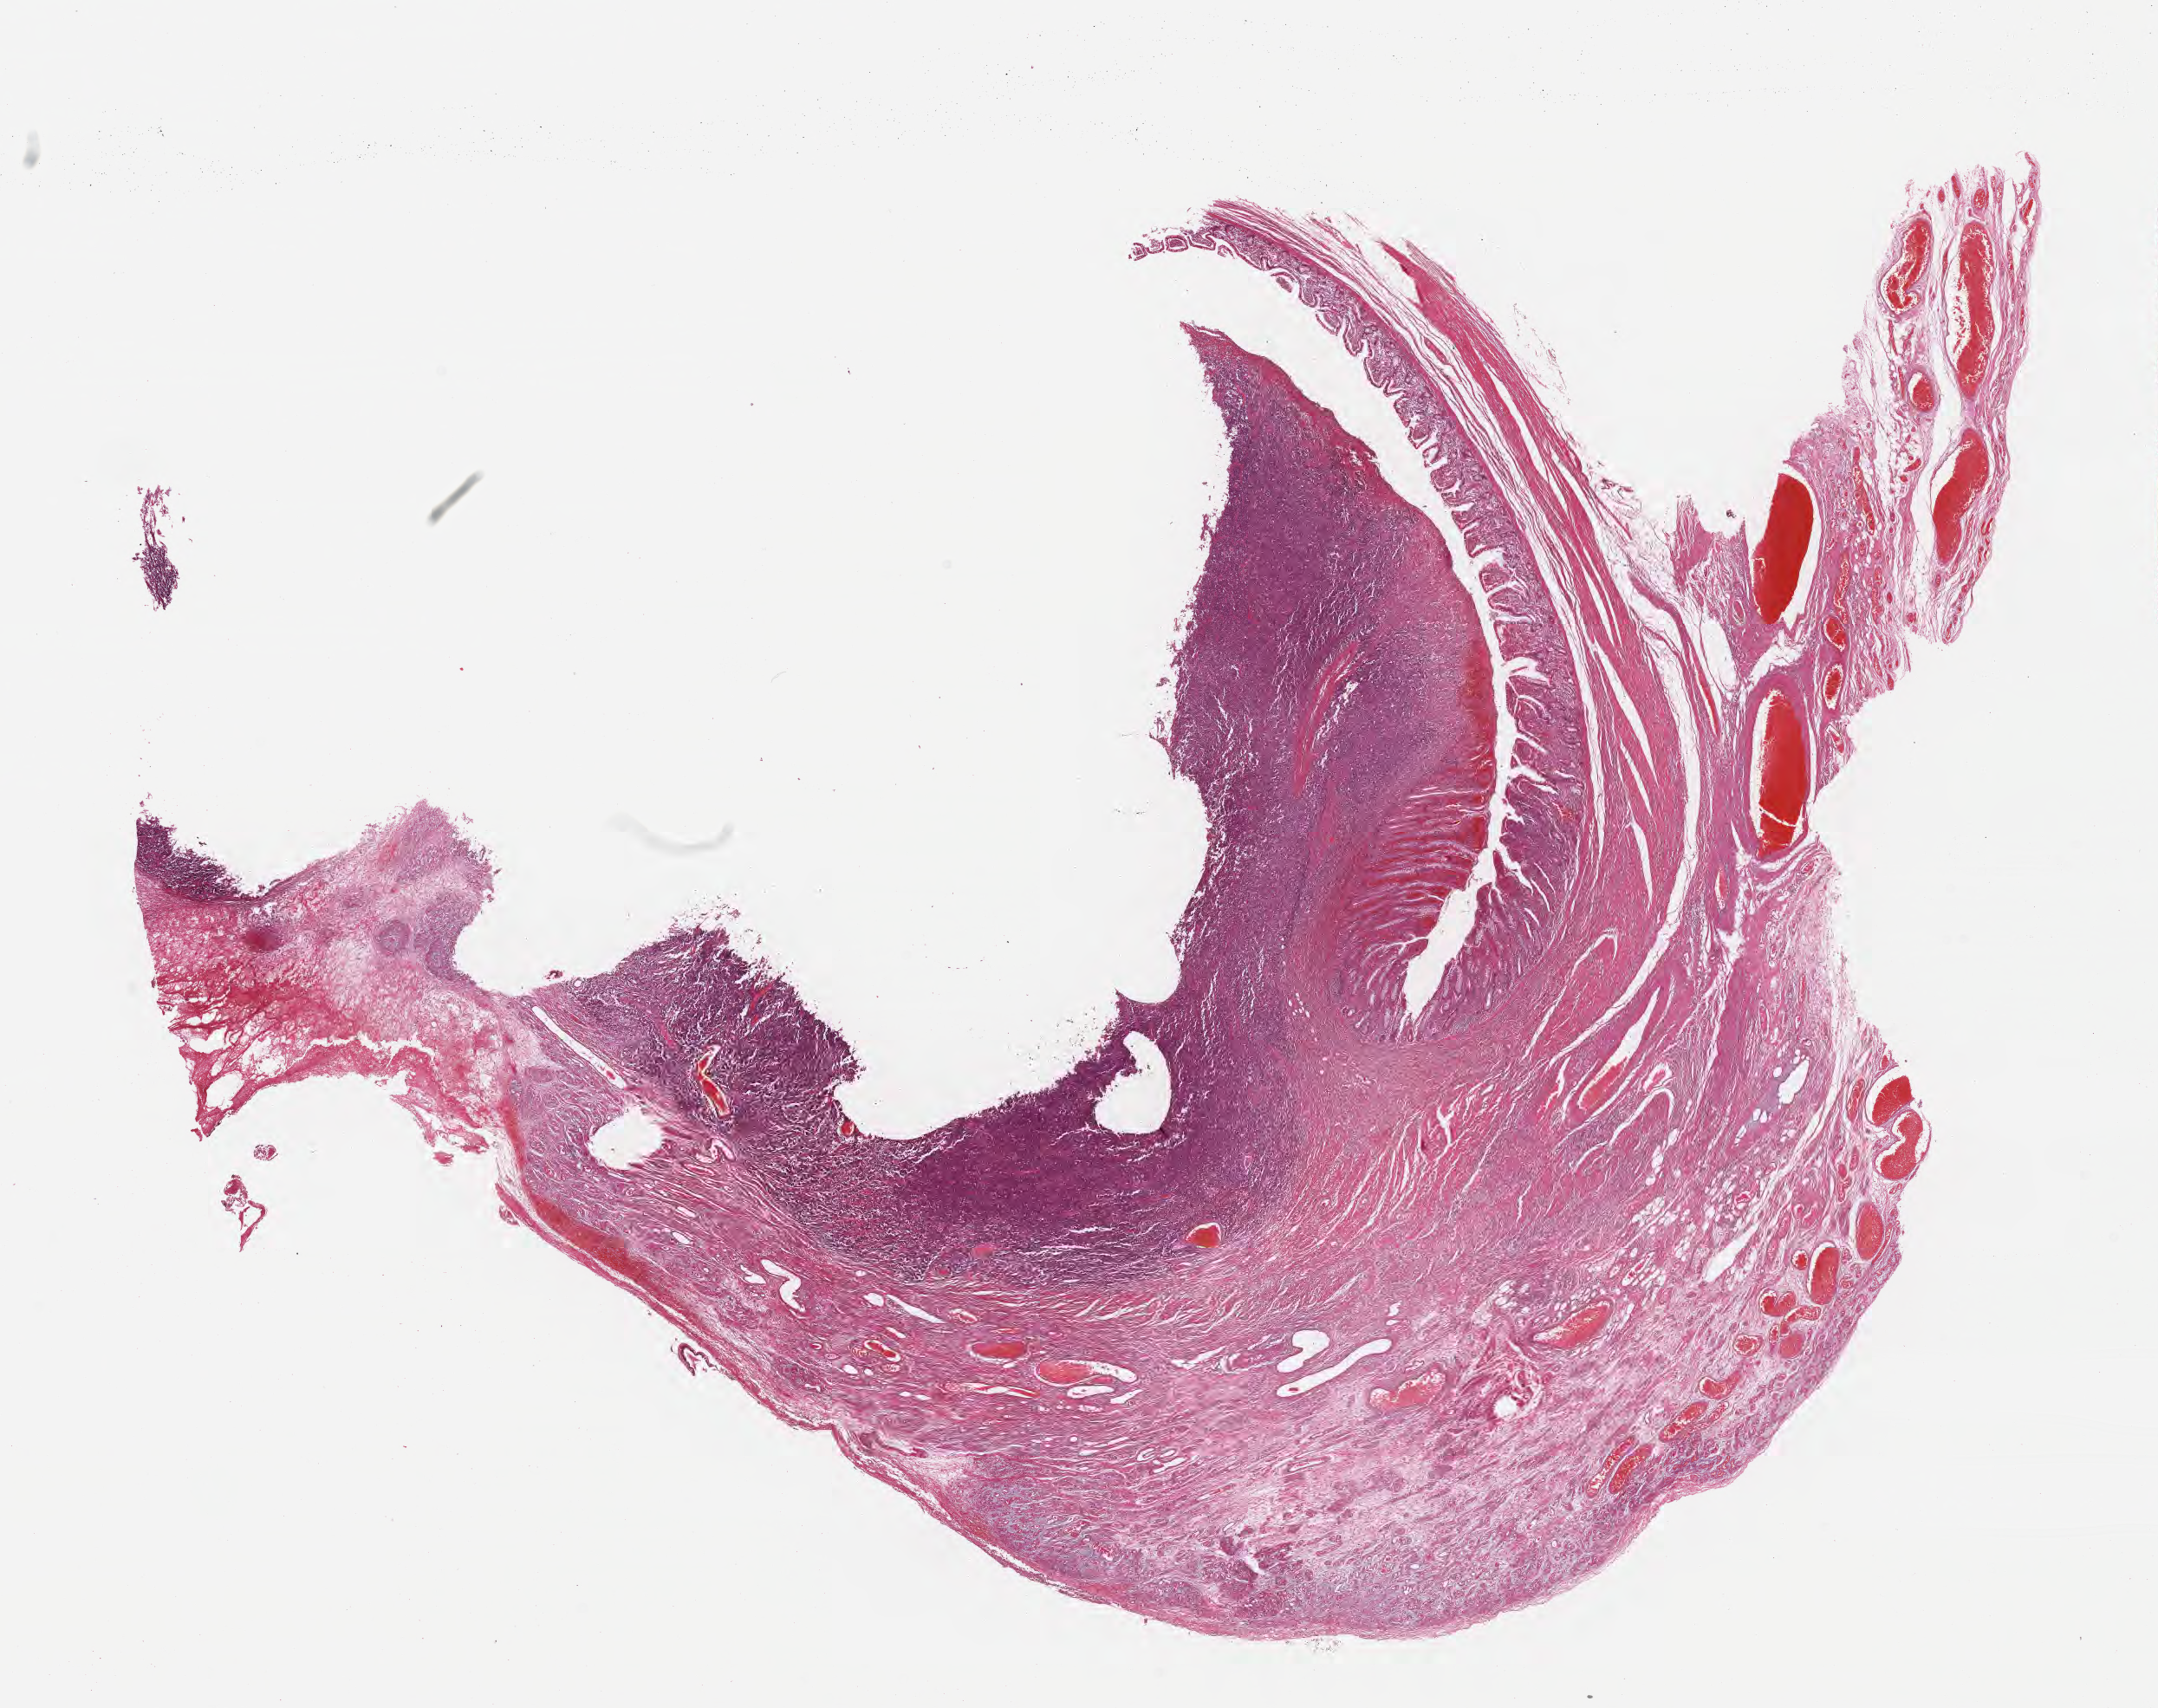
H&E whole-slide image, low-resolution overview of the scanned area, about 20.1 x 15.9 mm. FFPE section. Specimen: primary tumor. Male patient, aged 26. Pathologist review of this section (percent, as recorded): tumor cells 35%, tumor nuclei 50%, stromal cells 55%, necrosis 0%, normal cells 10%. Infiltration values recorded for this section: lymphocyte infiltration 60%, monocyte infiltration 20%, neutrophil infiltration 5%.
• section: top of the tissue portion
• histologic diagnosis: Burkitt lymphoma, NOS
• Ann Arbor stage (patient): Stage IV